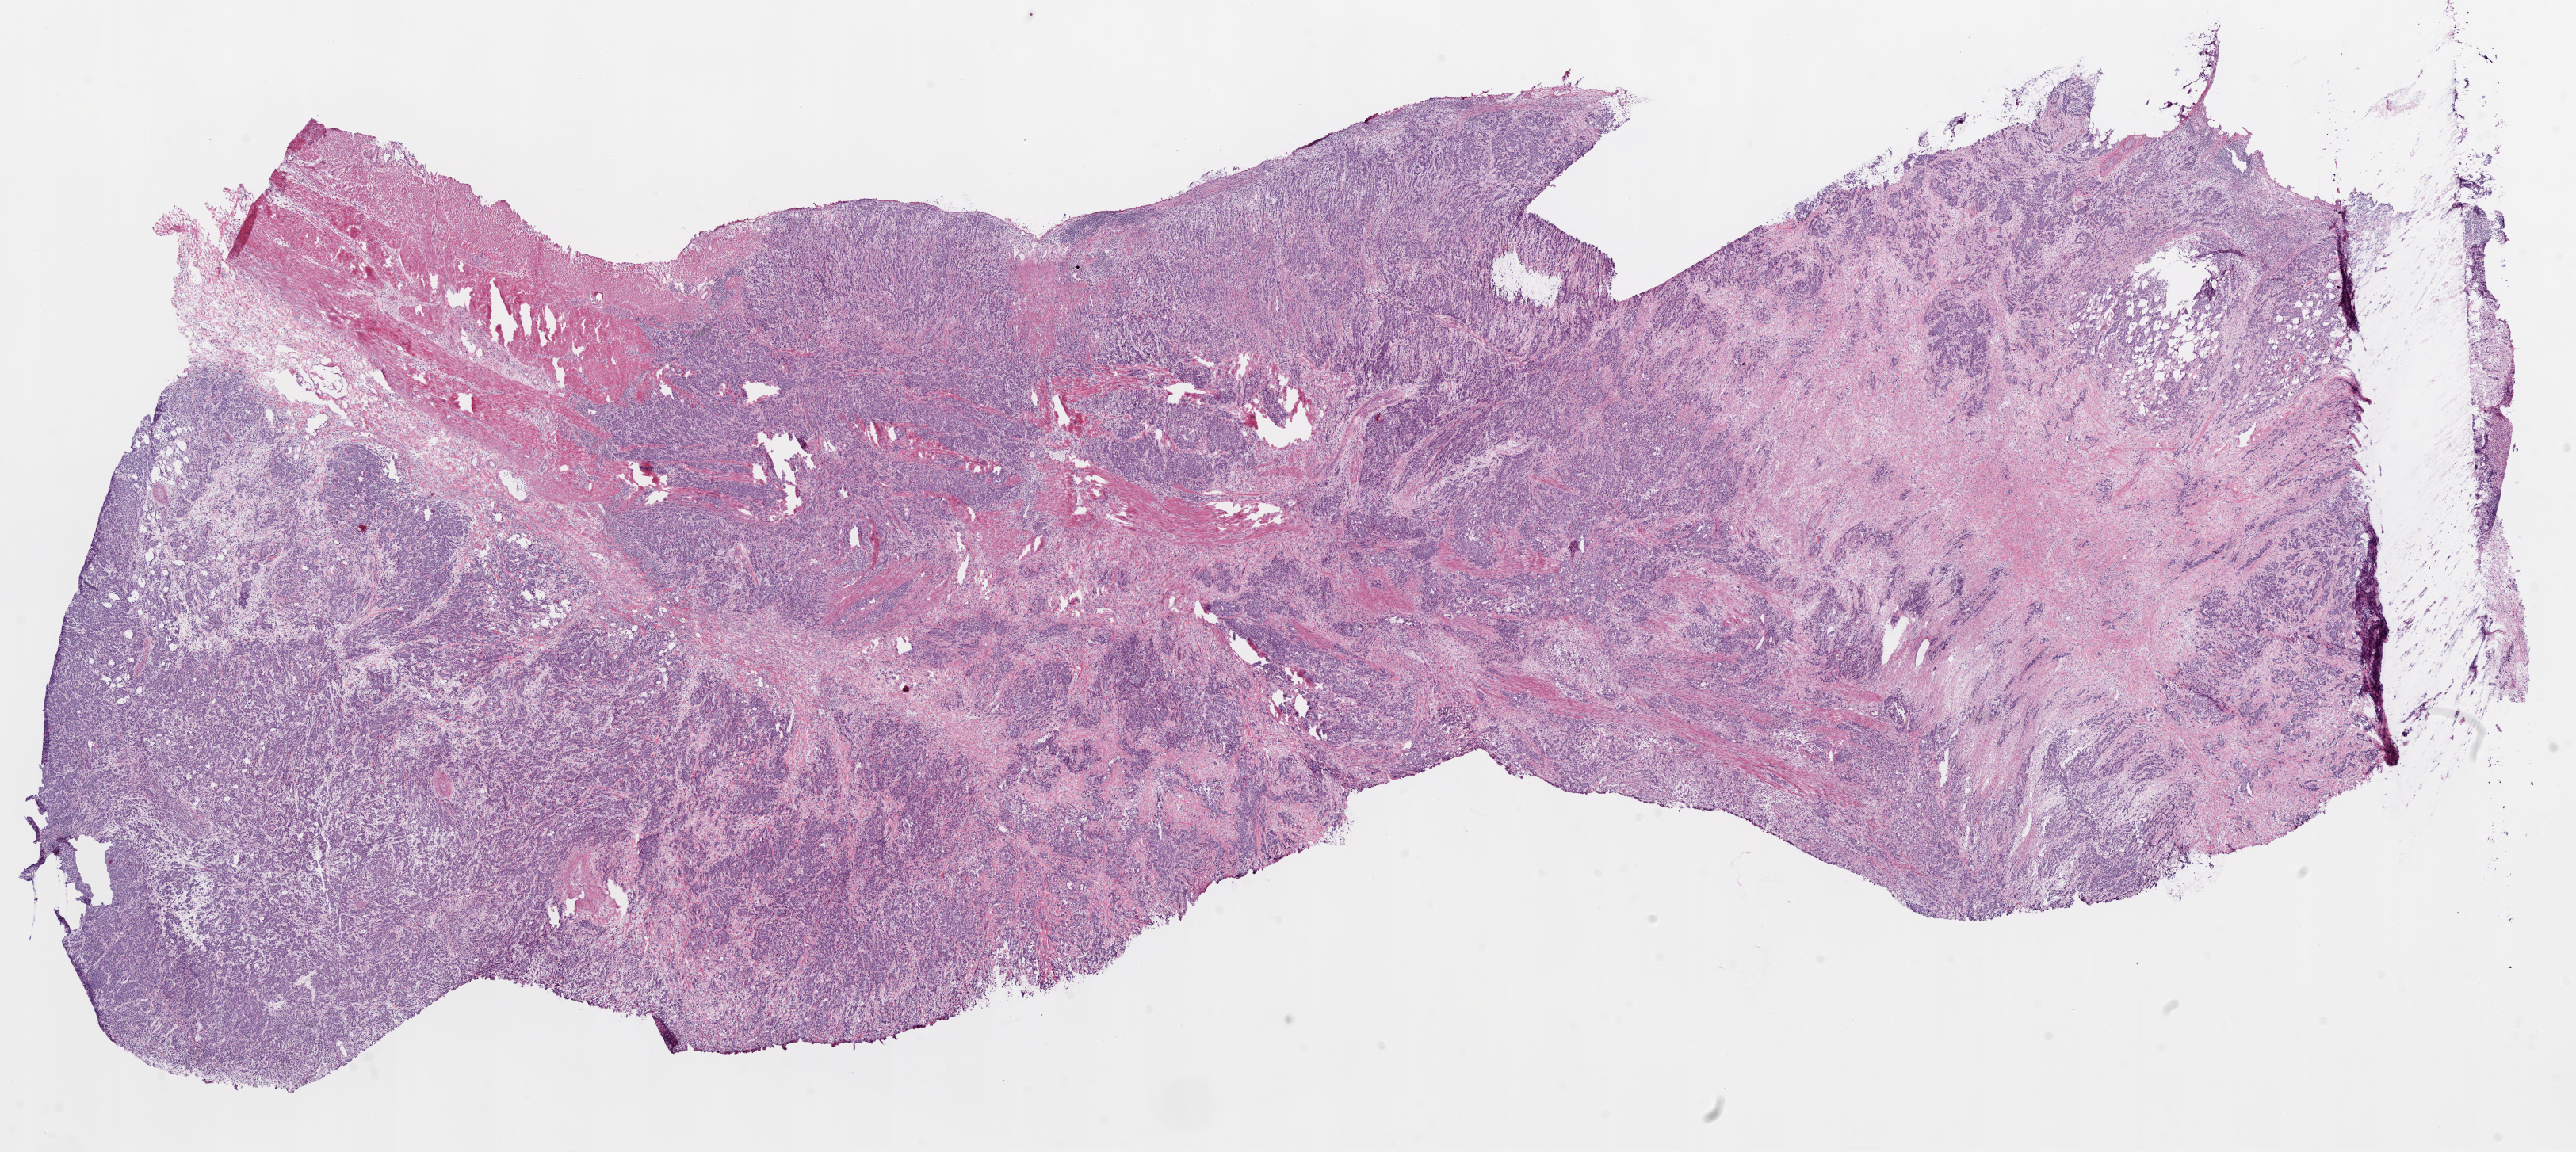
Whole-slide histology image, H&E-stained, low-resolution overview of the scanned area, about 26.1 x 11.7 mm, frozen section from the top of the tissue portion, sample: primary tumour, stomach. Female patient; age at initial diagnosis 66 years. Slide review estimates, as recorded: tumour cells 69%, tumour nuclei 80%.
Pathologic diagnosis: Adenocarcinoma, NOS.